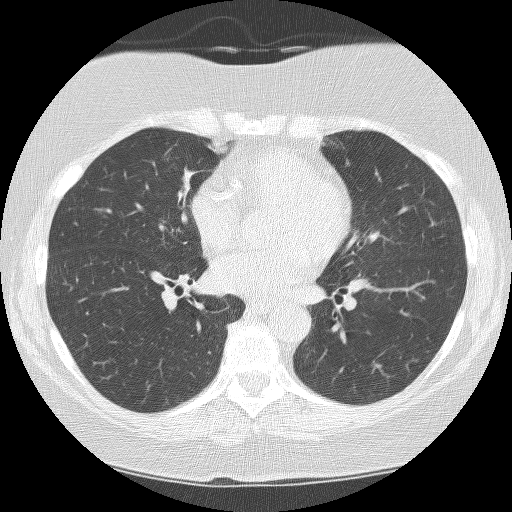
Low-dose screening chest CT, one axial slice. Reconstruction kernel BONE. 120 kVp. Lung window (W 1500 / L -600 HU). 2.5 mm slice thickness. 512 × 512 image matrix, field of view 299 × 299 mm.
Outlined on this slice (expert manual segmentation):
- lesion 1 (tumor, hilum of right lung): bounding box <176,167,195,210> (left, top, right, bottom; pixels)